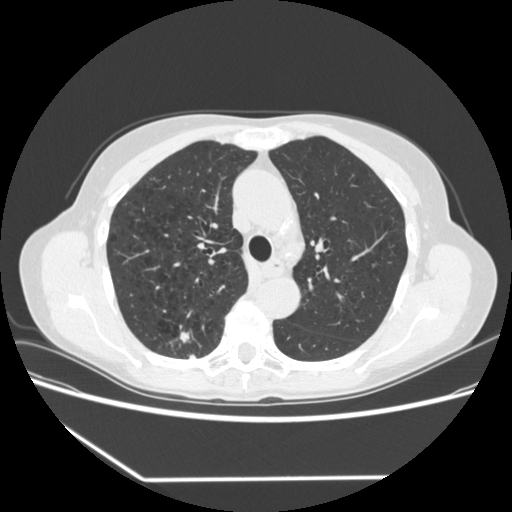
Low-dose screening chest CT, axial slice. Baseline annual screen. Lung window (W 1500 / L -600 HU). 1.25 mm slice thickness. 120 kVp. Slice 234 of 323 in the series. 512 × 512 image matrix, field of view 360 × 360 mm. Female, age 67 years at enrolment. Current smoker at enrolment.
- Lesion marked by an expert reader, box from (x=159, y=325) to (x=202, y=364) px.
- The screening reader recorded 2 non-calcified nodules or masses ≥4 mm on this exam; which of them this box marks is not recorded.
- Official screen result: positive, change unspecified: nodule(s) >= 4 mm or enlarging nodule(s), mass(es), or other non-specific abnormalities suspicious for lung cancer.
- Later outcome: lung cancer diagnosed 29 days after this screen — adenocarcinoma, NOS, right upper lobe, moderately differentiated (G2), stage IA (AJCC 6th edition), 24 mm at pathology.